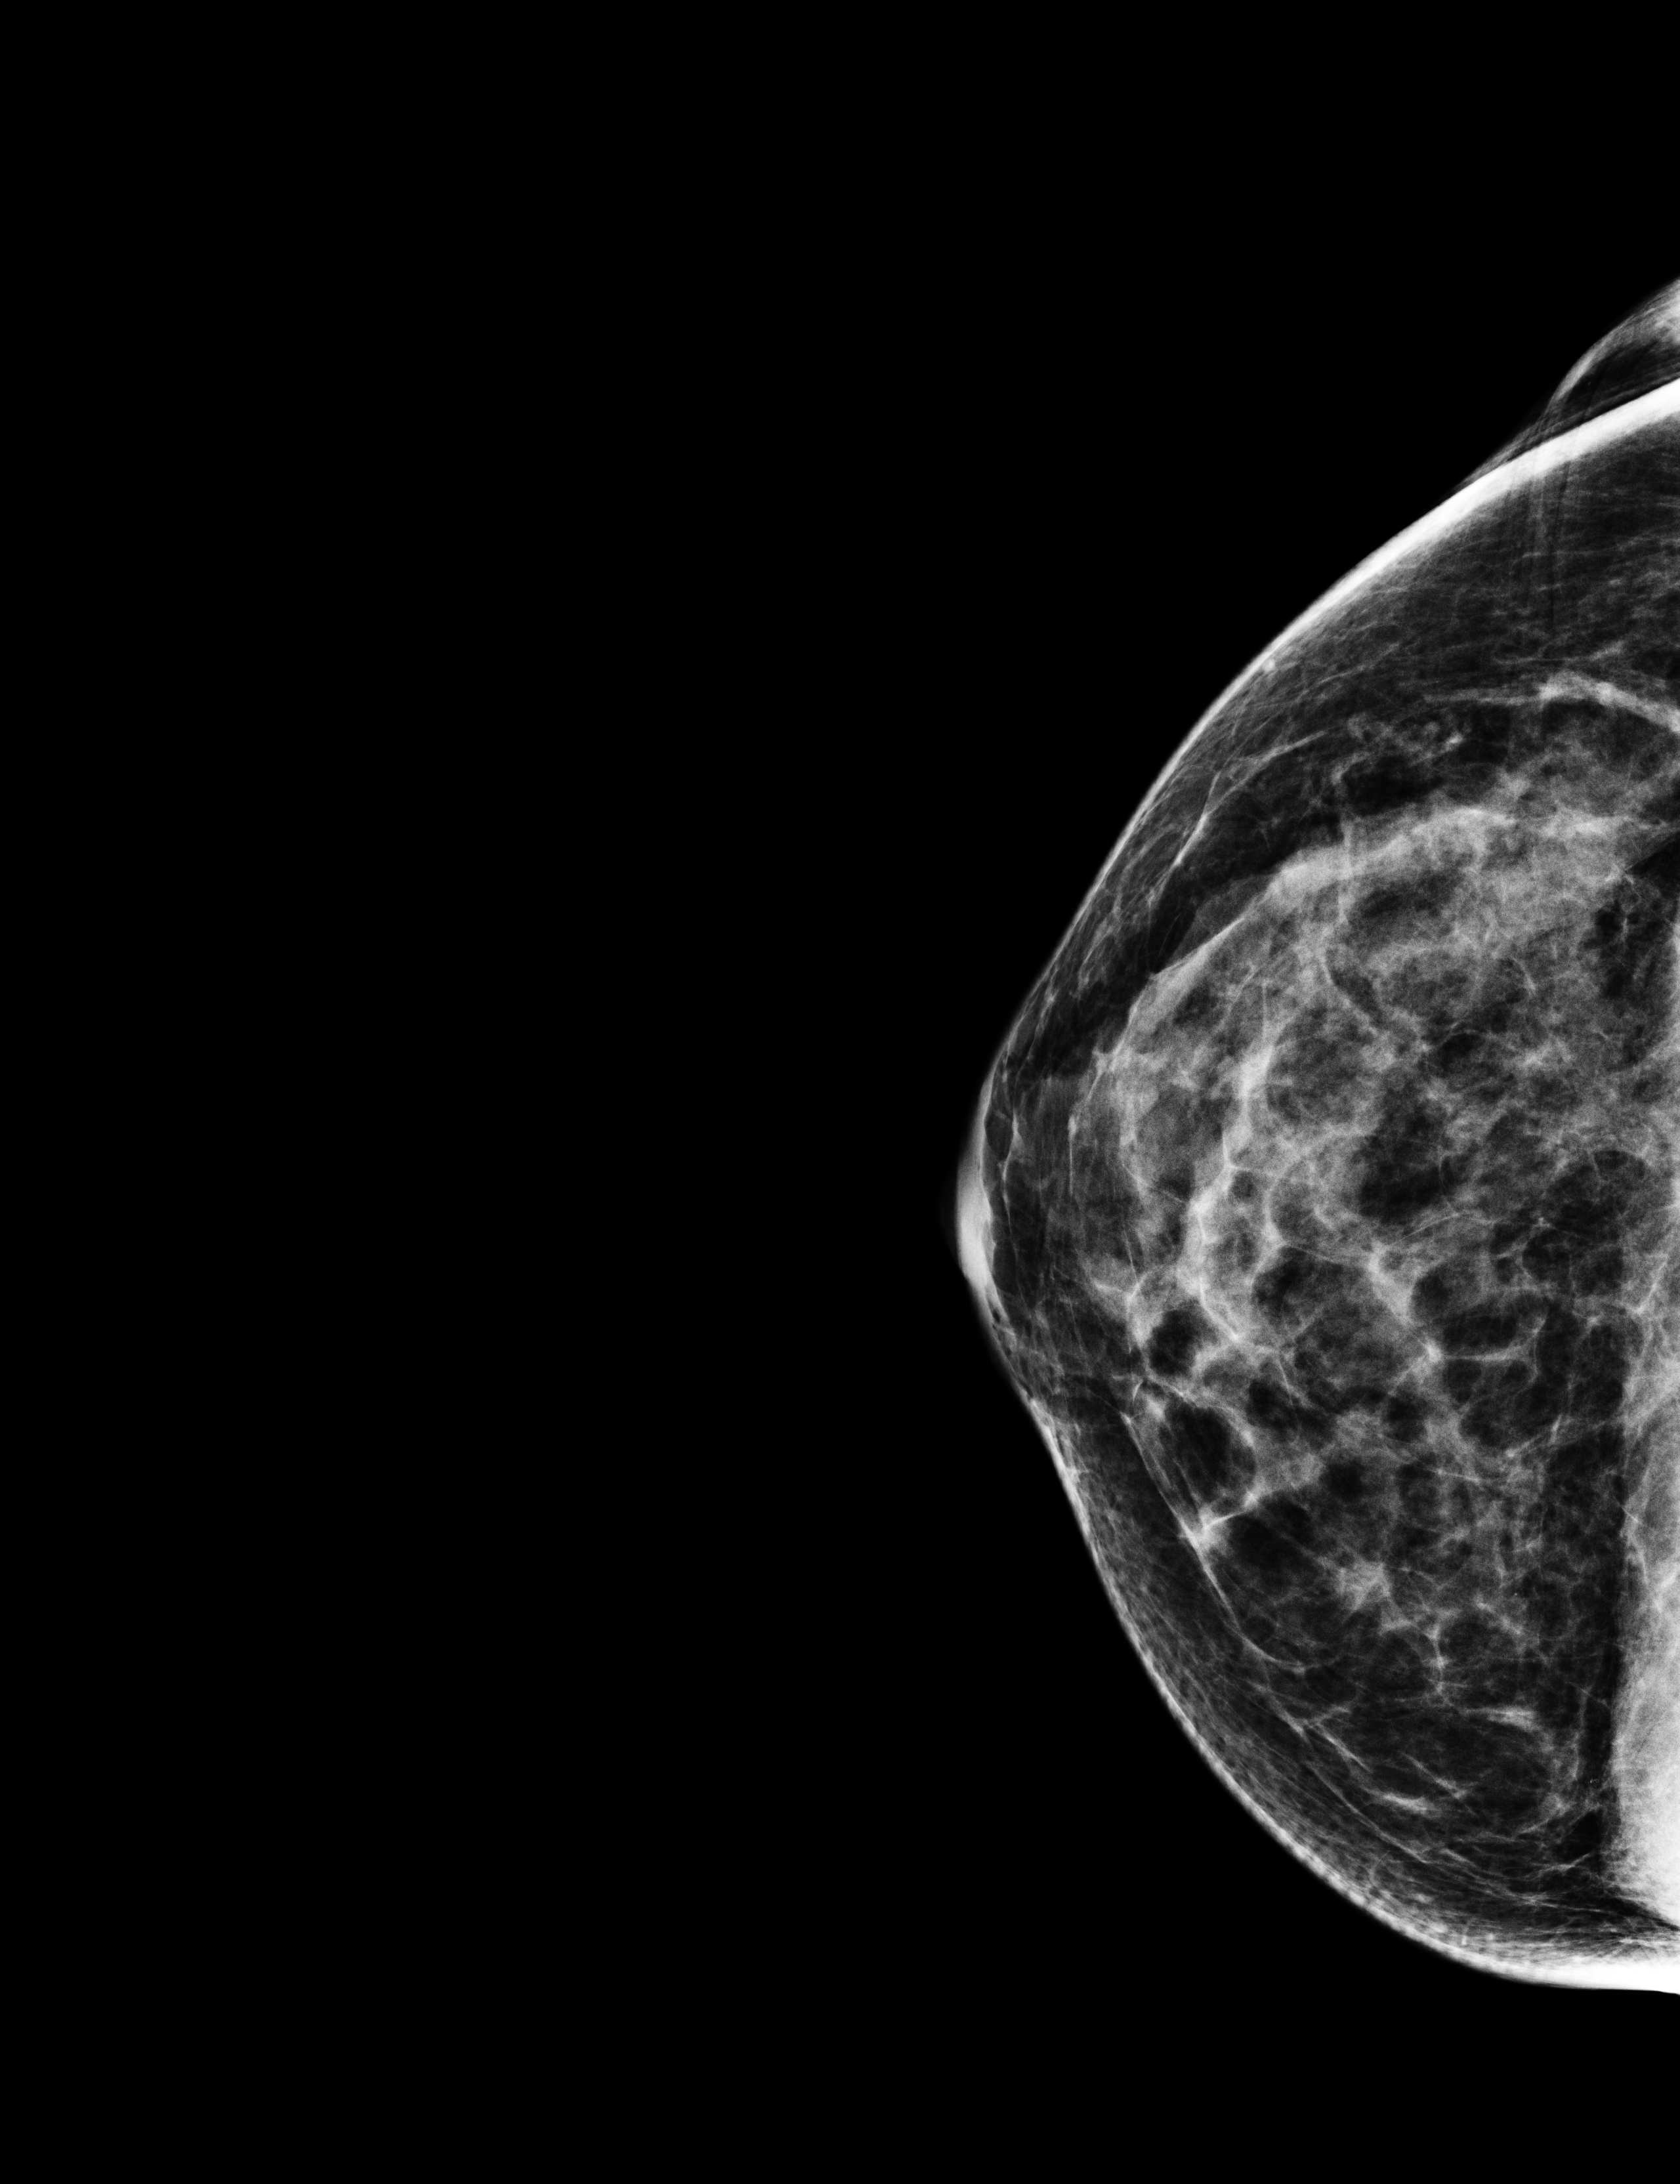
Screening examination, compressed breast thickness 48 mm.
Image type: full-field digital mammogram. Breast: right. Projection: craniocaudal (CC) view.